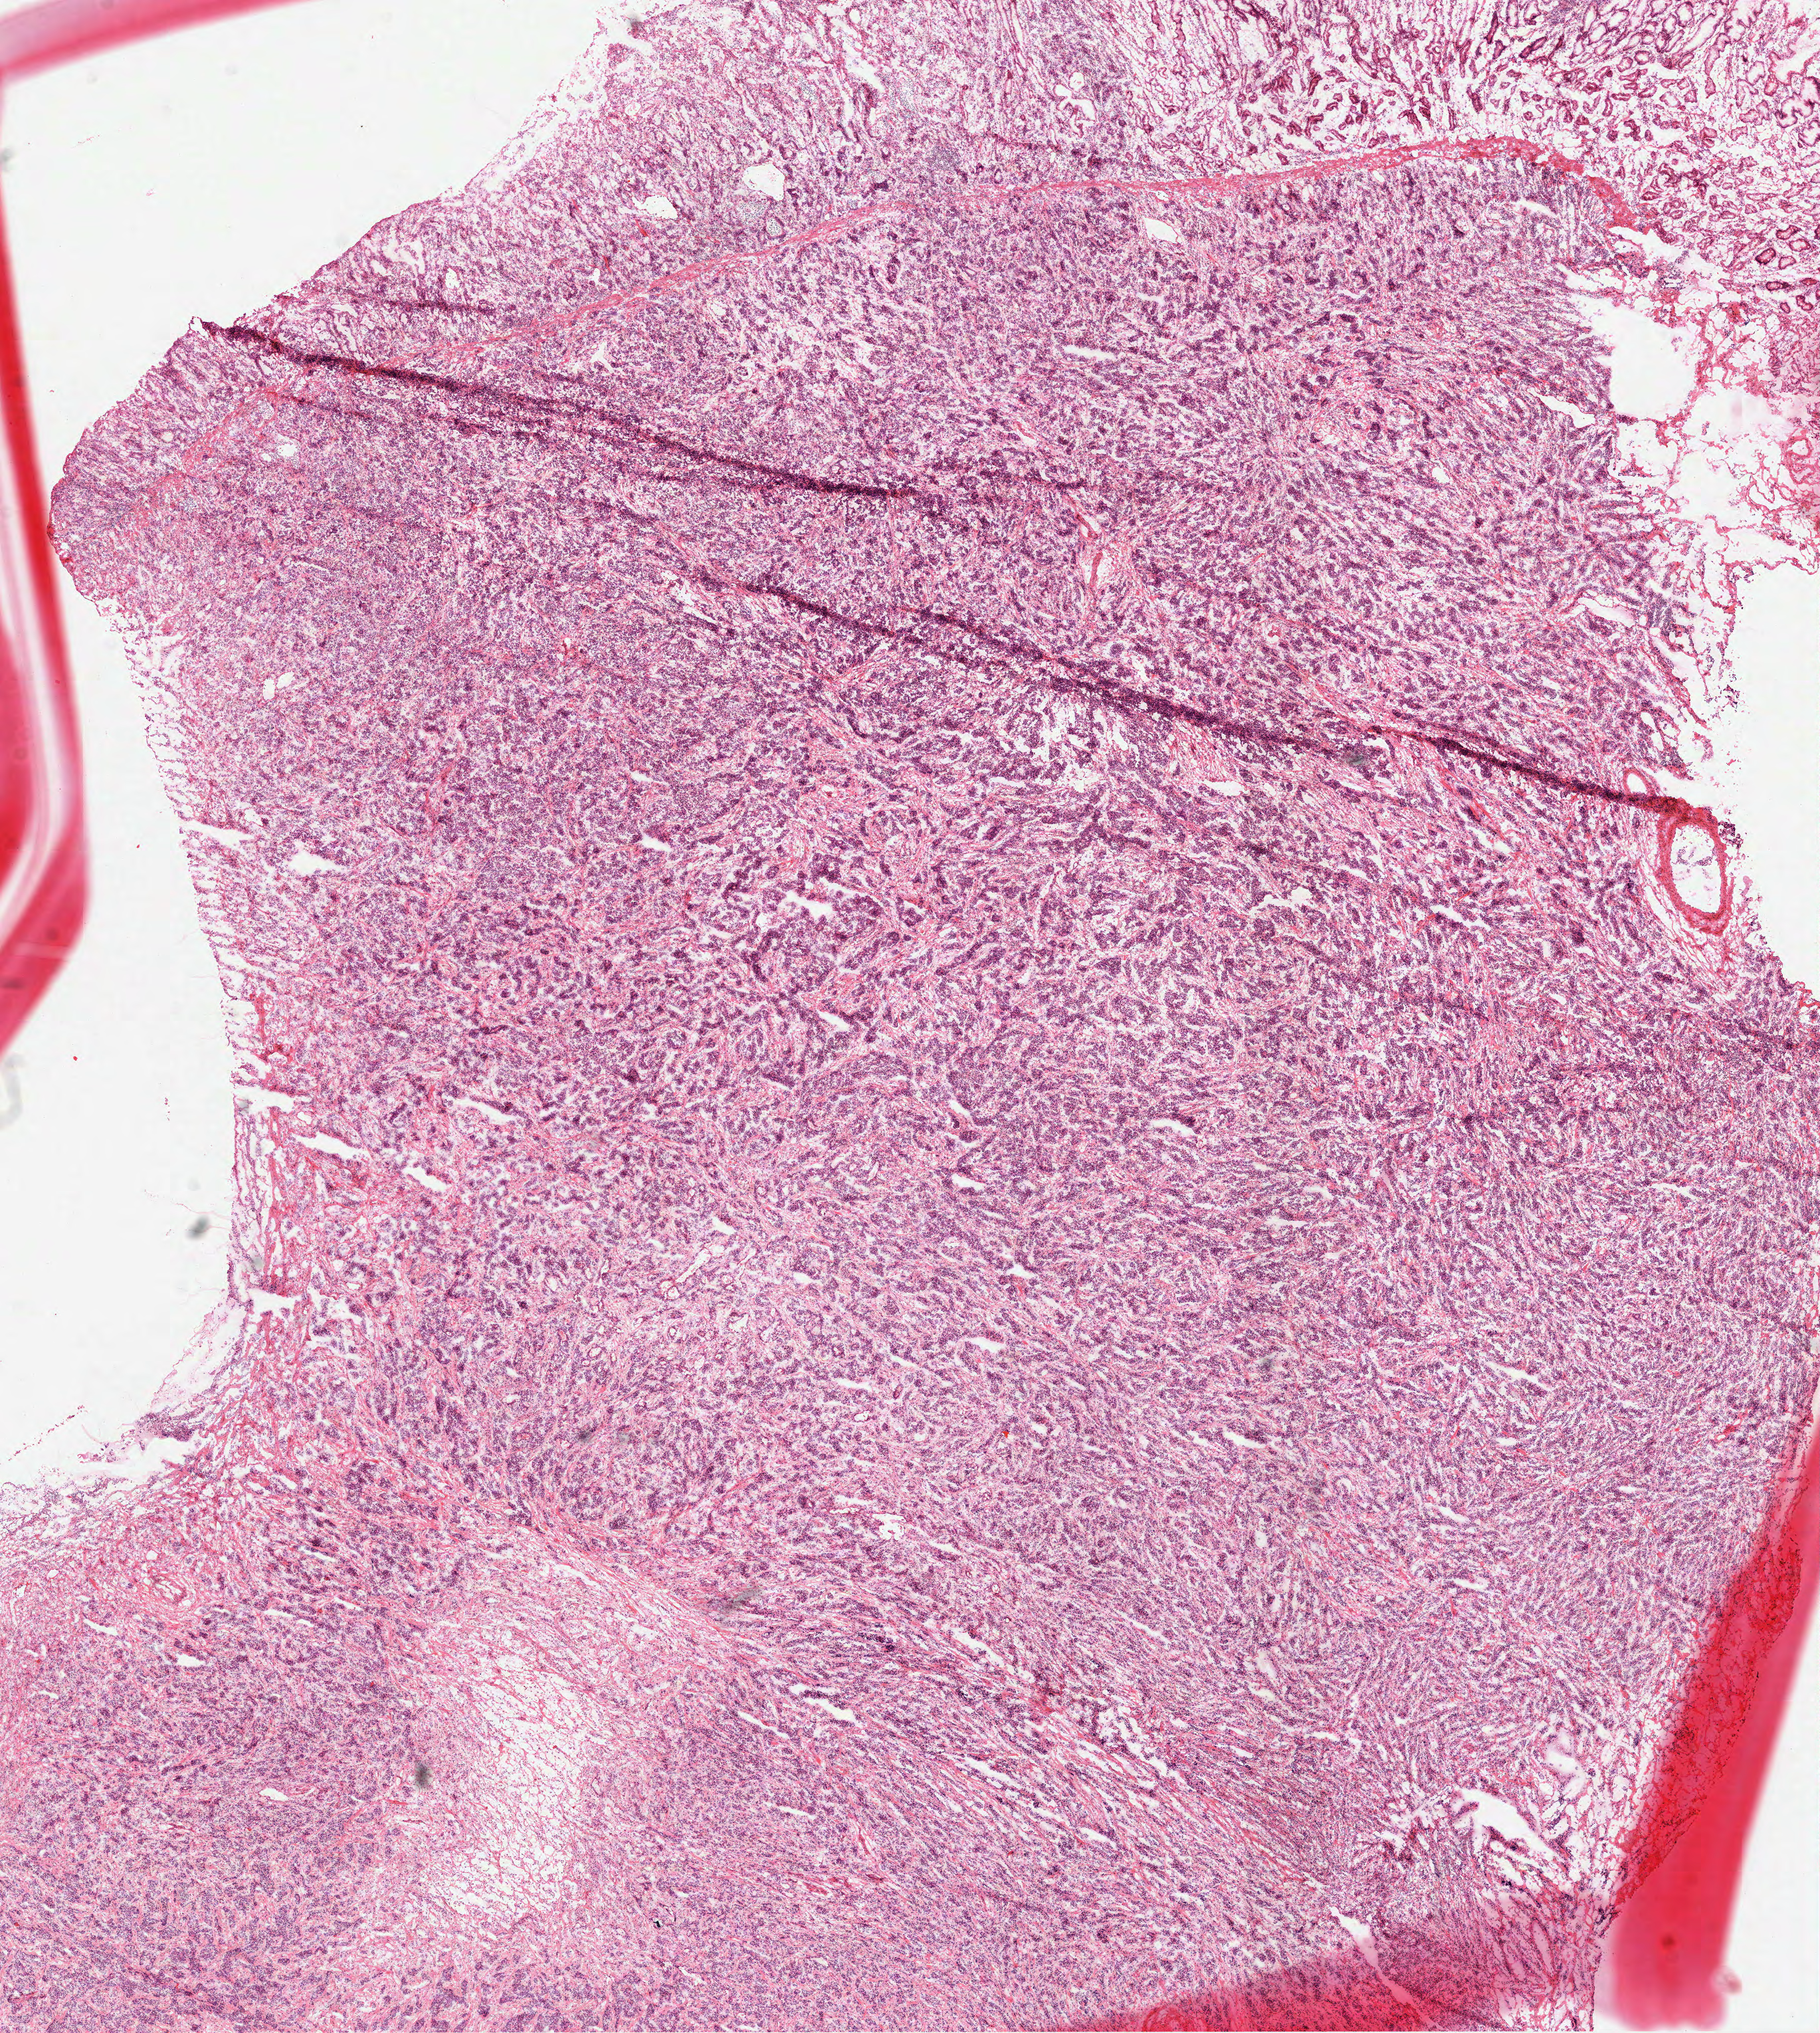
Whole-slide histology image, H&E, shown as a low-resolution overview of the whole scanned area (about 11.0 x 12.3 mm, acquisition: 40x scan), frozen section from the top of the tissue portion, sample: primary tumour, stomach. Male patient; age at initial diagnosis 59 years. Histologic grade: G3 (poorly differentiated). Slide review estimates, as recorded: tumour cells 100%, tumour nuclei 80%, normal cells 0%, stromal cells 0%, necrosis 0%. Inflammatory infiltration, as recorded: lymphocyte infiltration 5%, monocyte infiltration 0%, neutrophil infiltration 2%.
- AJCC pathologic stage: IIB
- histologic diagnosis: Adenocarcinoma, NOS (body of stomach)